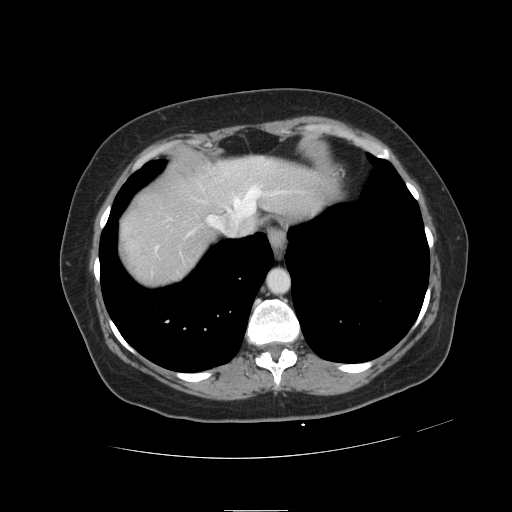
Contrast-enhanced abdominal CT, one axial slice; position 105 of 121 along the scan axis; 120 kVp; intravenous contrast given; soft-tissue window (W 400 / L 40 HU); 2.5 mm slice thickness; 512 × 512 image matrix, field of view 400 × 400 mm. Female patient, age 52 years. Case-level facts recorded for this patient, not image findings: diagnosis: colorectal cancer liver metastases, imaged before liver resection; multiple liver metastases: yes; largest metastasis: 6.3 cm.
Structures marked on this image (expert manual segmentation):
- hepatic veins: bounding box (x1, y1, x2, y2) in pixels: (155, 186, 288, 251)
- liver: (119, 157, 327, 286)
- planned liver remnant (the part of the liver to remain after resection): (191, 156, 328, 215)